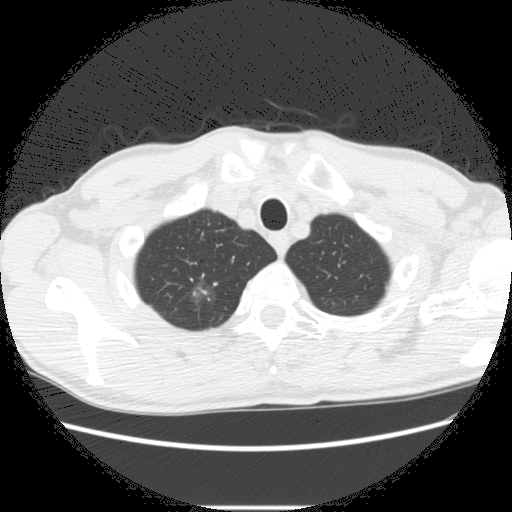
Chest CT (low-dose screening protocol), one axial image, second annual screen, lung window (W 1500 / L -600 HU), 2.5 mm slice thickness, standard (soft-tissue) reconstruction kernel (STANDARD). Male, age 66 years at enrolment.
Expert reader's lesion annotation, bounding box [x1, y1, x2, y2] px = [173, 280, 231, 326]. The screening reader recorded 5 non-calcified nodules or masses ≥4 mm on this exam (right lower lobe, right upper lobe, right upper lobe, right upper lobe, left lower lobe); which of them this box marks is not recorded. Participant outcome: lung cancer diagnosed 75 days after this screen — adenocarcinoma, NOS, right upper lobe, undifferentiated (G4), stage IA (AJCC 6th edition), 20 mm at pathology.